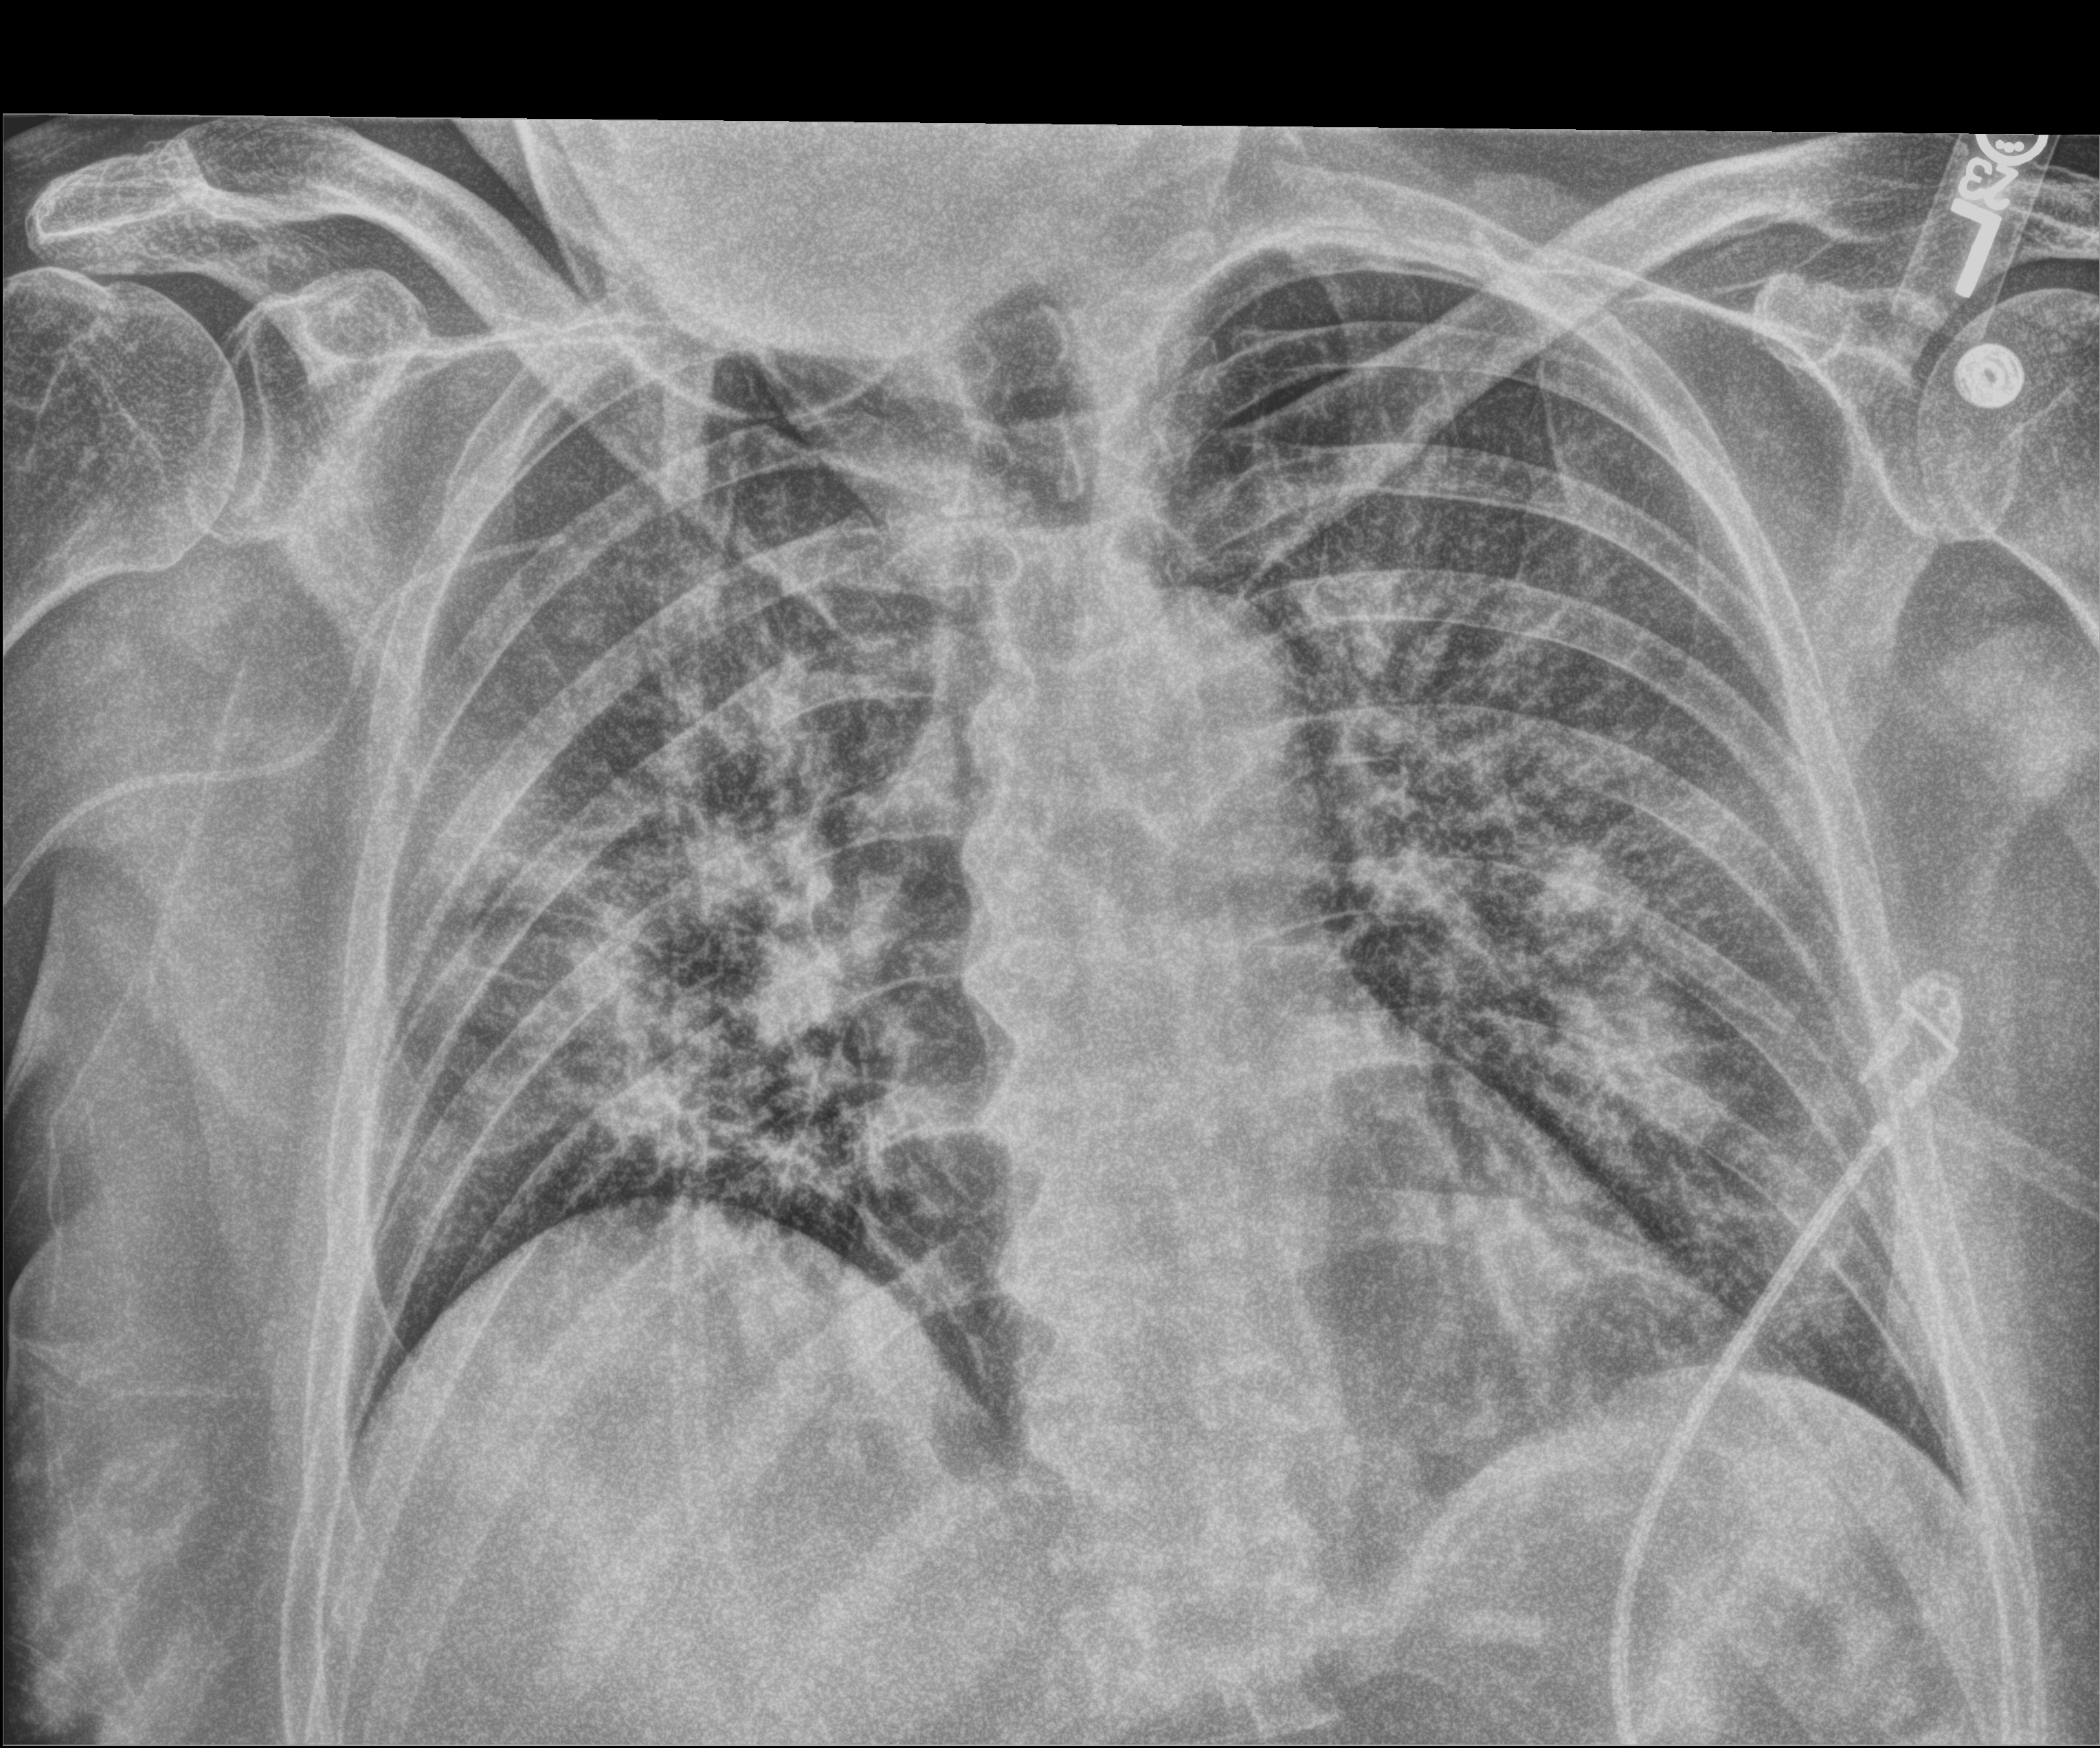
Portable chest radiograph; anteroposterior (AP) projection. Male patient hospitalised with COVID-19, age 60–74 years.
Admission-level facts for this patient (not findings on this image; timing relative to this image not recorded):
- hypertension (admission record): no